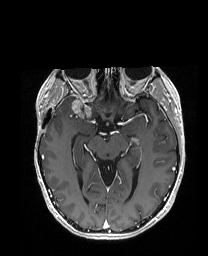
Brain MRI from a brain-tumour surgery series, one axial slice; slice 106 of 192 in the series (ordered by position); T1-weighted post-contrast; 1 mm slice thickness; 208 × 256 image matrix, field of view 203 × 250 mm. Case-level facts recorded for this patient, not image findings: histopathology: Metastatic Carcinoma from Breast primary; tumour location: Right Frontal.
Structures marked on this image (manually delineated by an expert):
- tumour: bounding box <61,97,81,115> (left, top, right, bottom; pixels)